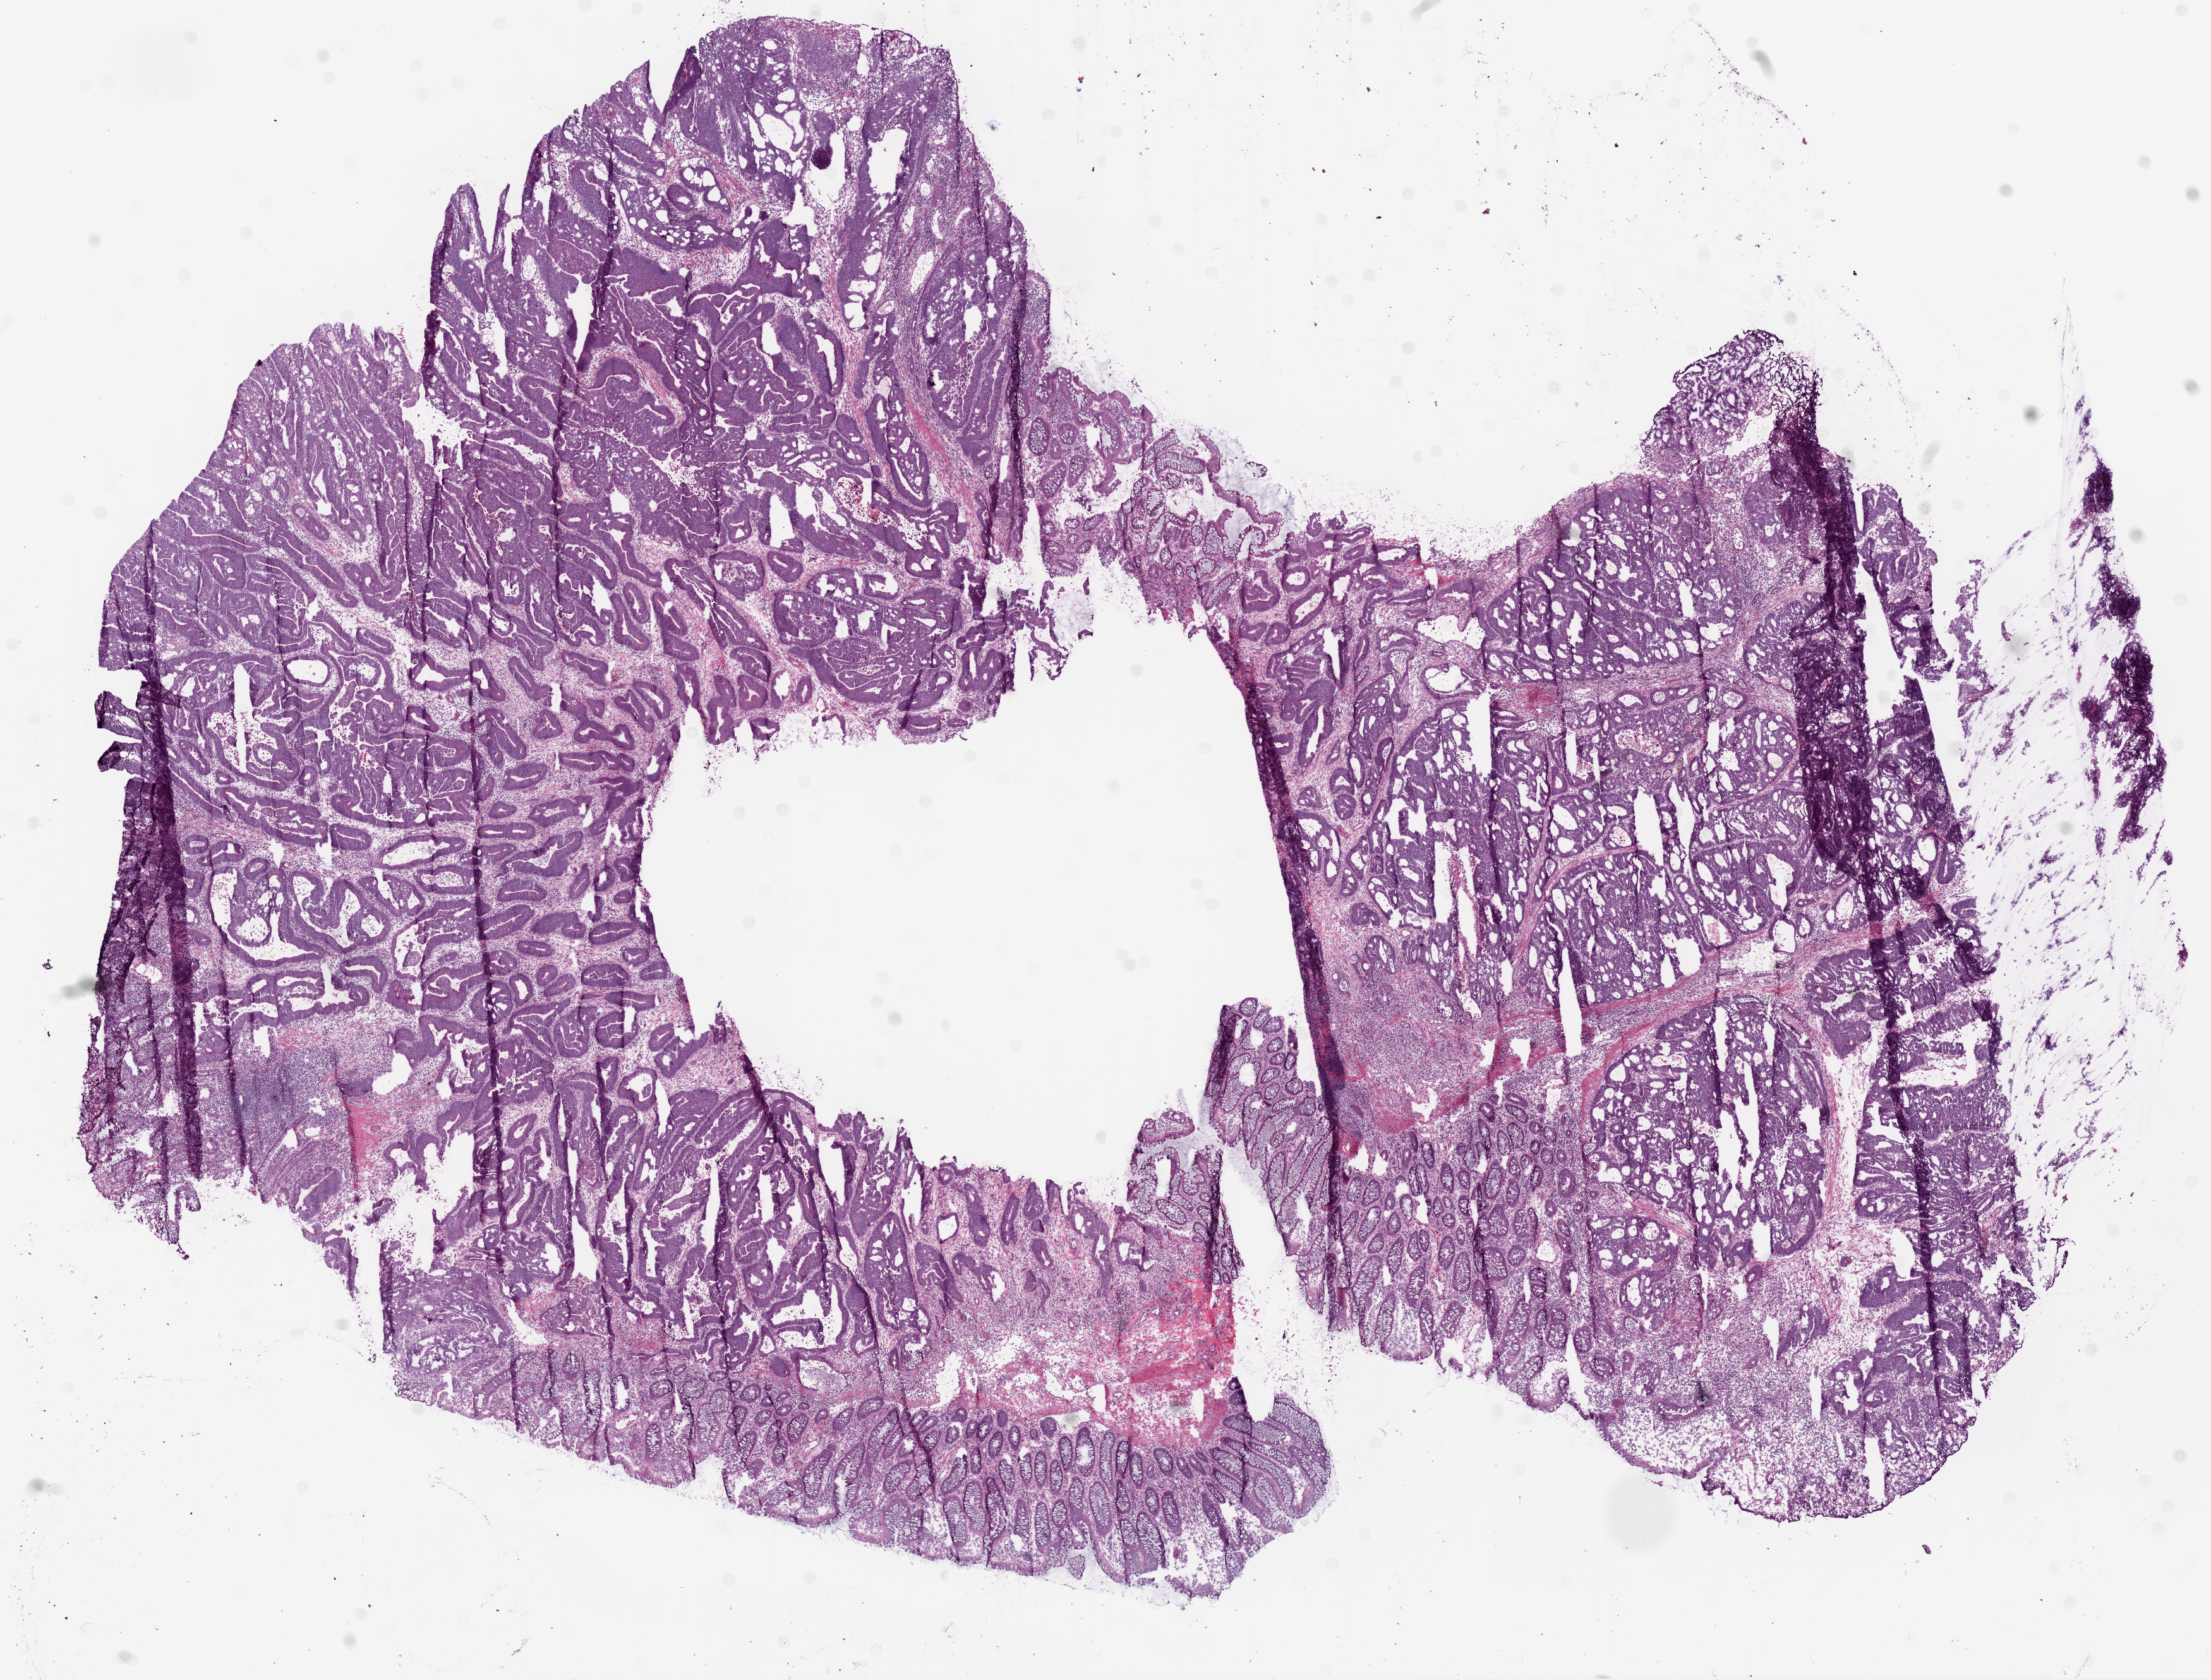
H&E-stained whole-slide image, whole scanned area (about 14.0 x 10.7 mm) shown as a low-resolution overview; frozen section from the bottom of the tissue portion; rectum, primary tumour sample. Male, age 75 years at initial diagnosis. Pathologist review of this section (percent, as recorded): tumour cells 83%, tumour nuclei 65%.
Pathologic diagnosis: Adenocarcinoma, NOS (rectosigmoid junction).